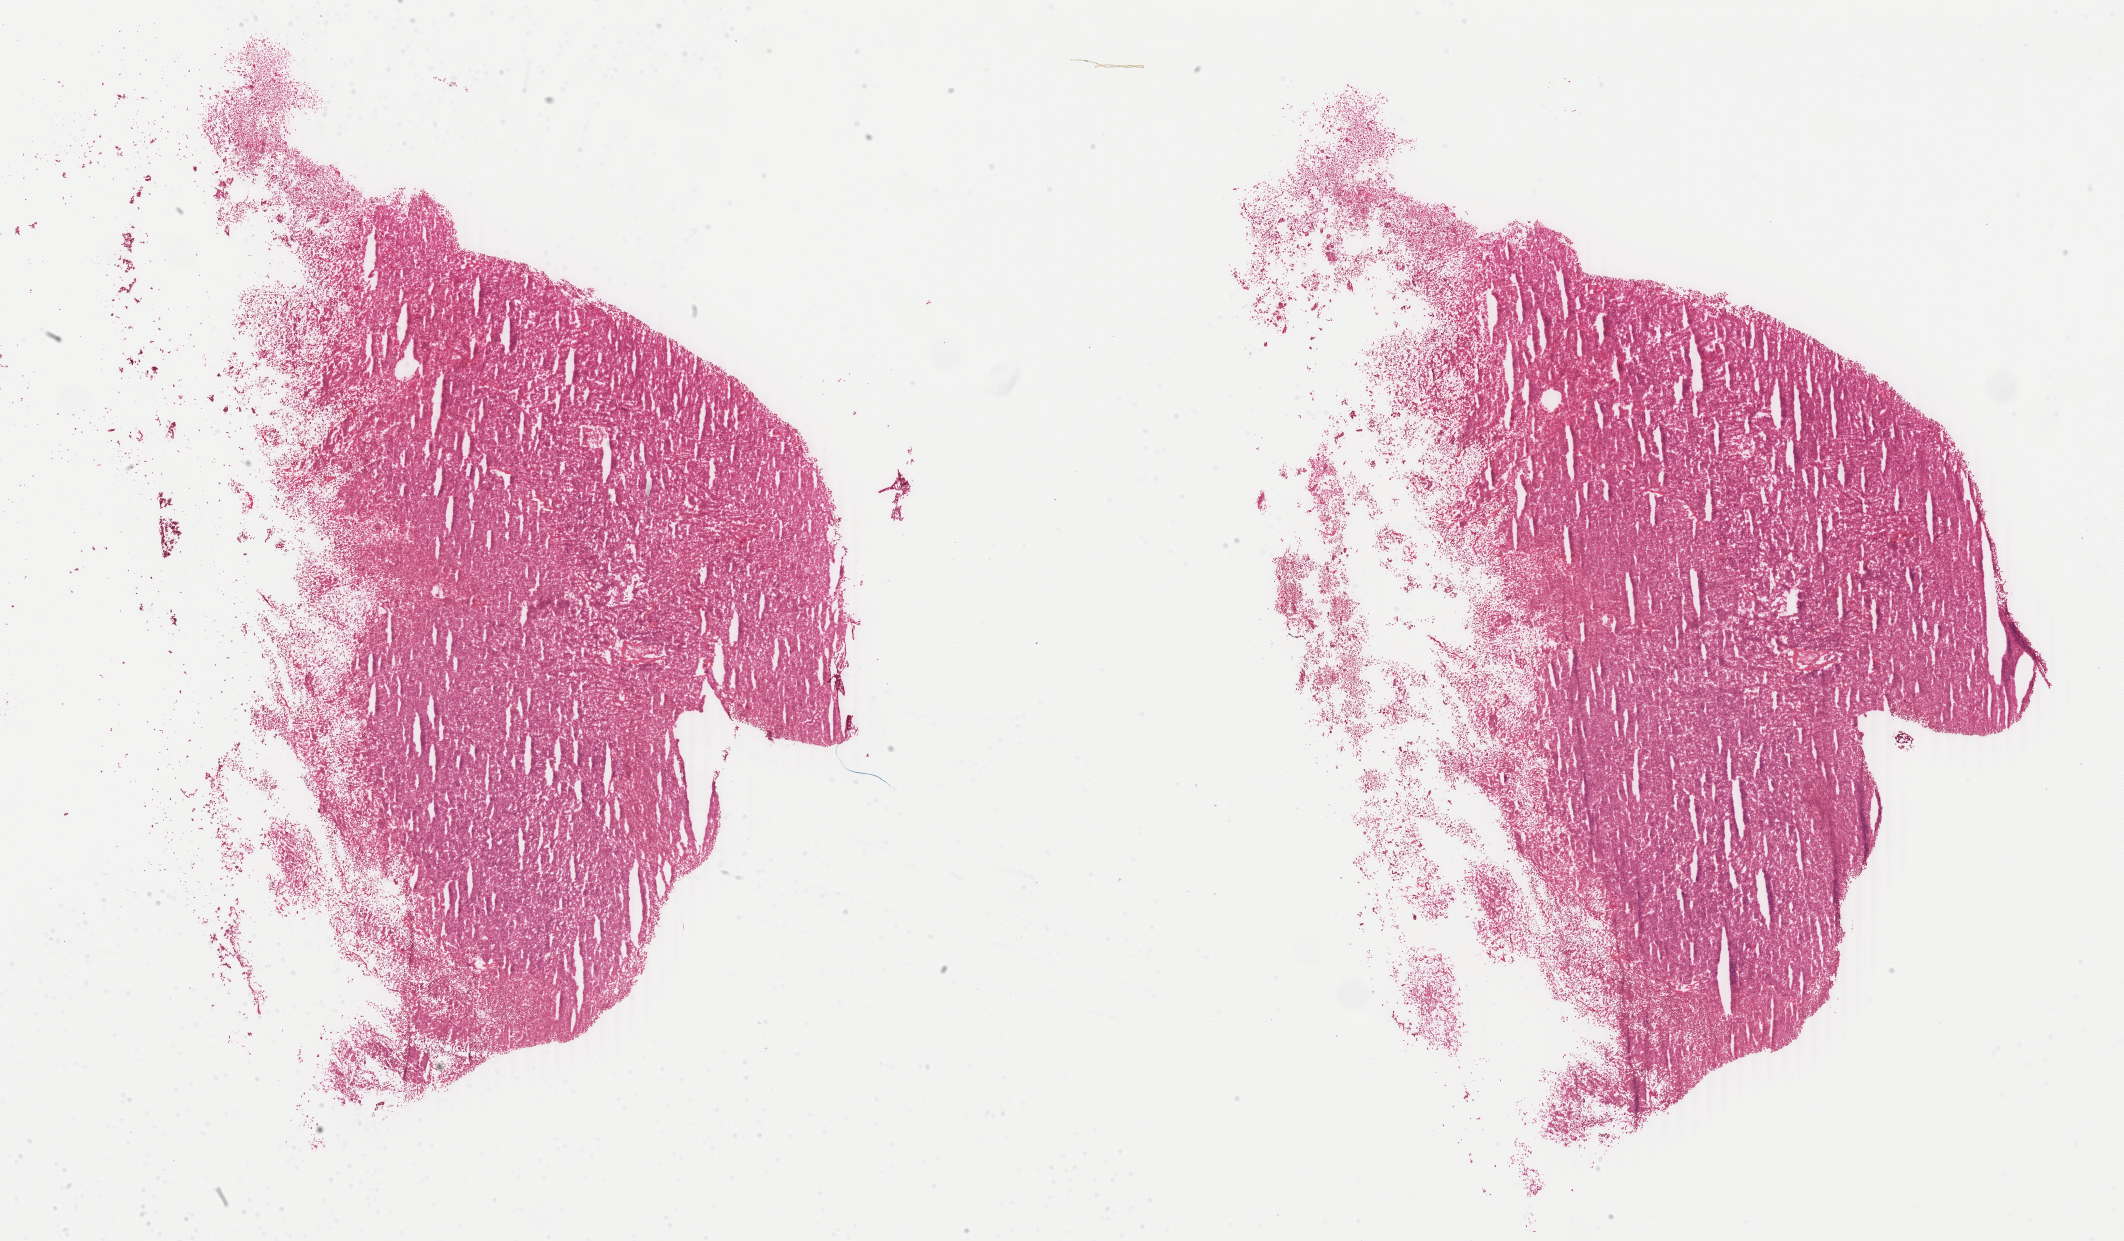
Whole-slide histology image, H&E-stained, a low-resolution overview of the entire scanned area, about 33.8 x 19.7 mm (from a 40x scan). Frozen section from the top of the tissue portion. Sample: primary tumour, kidney. Male patient; age at initial diagnosis 36 years. Composition of this section per pathologist review: tumour cells 85%, tumour nuclei 85%, normal cells 0%, stromal cells 15%, necrosis 0%. Infiltration values recorded for this section: lymphocyte infiltration 2%, monocyte infiltration 1%, neutrophil infiltration 1%.
* AJCC pathologic stage: I
* pathologic diagnosis: Renal cell carcinoma, chromophobe type